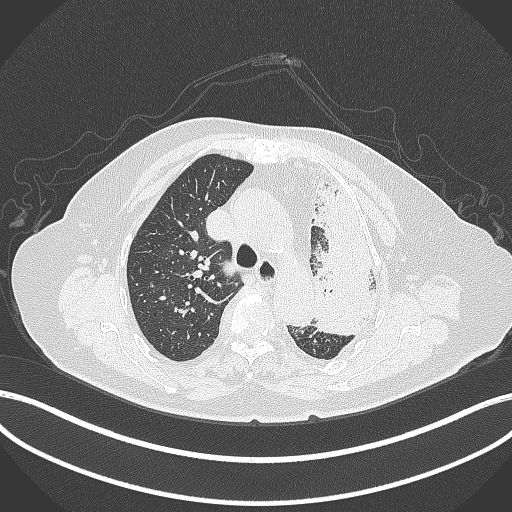
Chest CT, one axial slice. Reconstruction kernel B70f. 120 kVp. Lung window (W 1500 / L -600 HU). 1 mm slice thickness. 512 × 512 image matrix, field of view 400 × 400 mm. Female patient, age 75 years. From the clinical record (not read from this slice): clinical TNM (as recorded): T3 N3 M1.
Structures marked on this image (rectangle marked by the reading radiologist):
- lung tumour (recorded histology: adenocarcinoma): box from (x=301, y=168) to (x=390, y=338) px